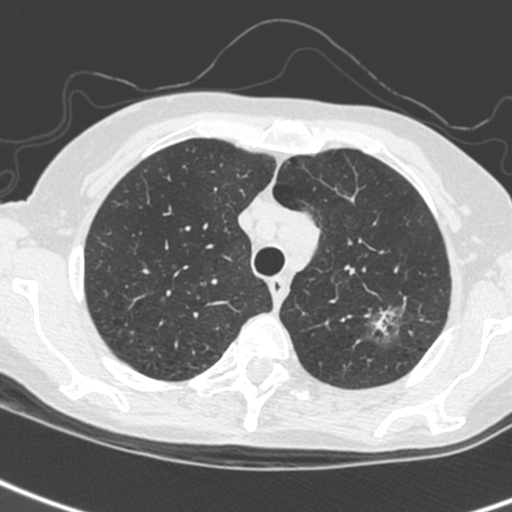
Axial slice from a low-dose chest CT screening exam; baseline screening round; lung window (W 1500 / L -600 HU); 1.3 mm slice thickness; standard (soft-tissue) reconstruction kernel (C); slice 40 of 242 in the series. Female, age 61 years at enrolment.
- Lesion marked by an expert reader, bounding box [x1, y1, x2, y2] px = [351, 302, 412, 351].
- The screening reader recorded 2 non-calcified nodules or masses ≥4 mm on this exam; which of them this box marks is not recorded.
- Participant outcome: lung cancer diagnosed 29 days after this screen — small cell carcinoma, NOS, left upper lobe, stage IV (AJCC 6th edition).